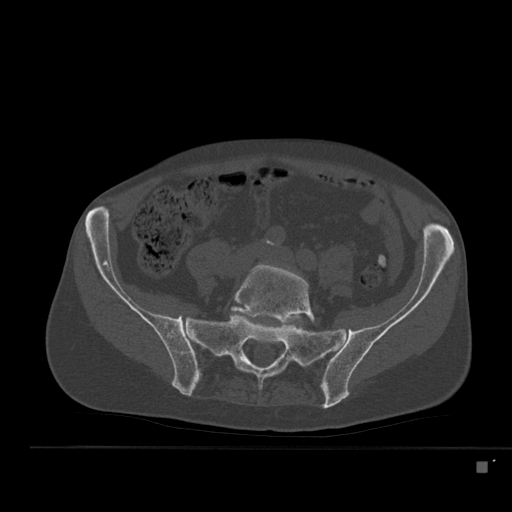
CT including the spine, one axial slice; position 116 of 517 along the scan axis; reconstruction kernel Br40s; 120 kVp; bone window (W 1800 / L 400 HU); 1.5 mm slice thickness; 512 × 512 image matrix. Patient: male, 70 years. From the clinical record (not read from this slice): primary cancer: renal; vertebrae with lytic lesions (as recorded): T4, T6, T10, T12, L3, L4, L5.
Annotated regions visible in this slice (semi-automatically segmented with operator editing):
- L5 vertebra: bounding box (x1, y1, x2, y2) in pixels: (228, 264, 315, 324)